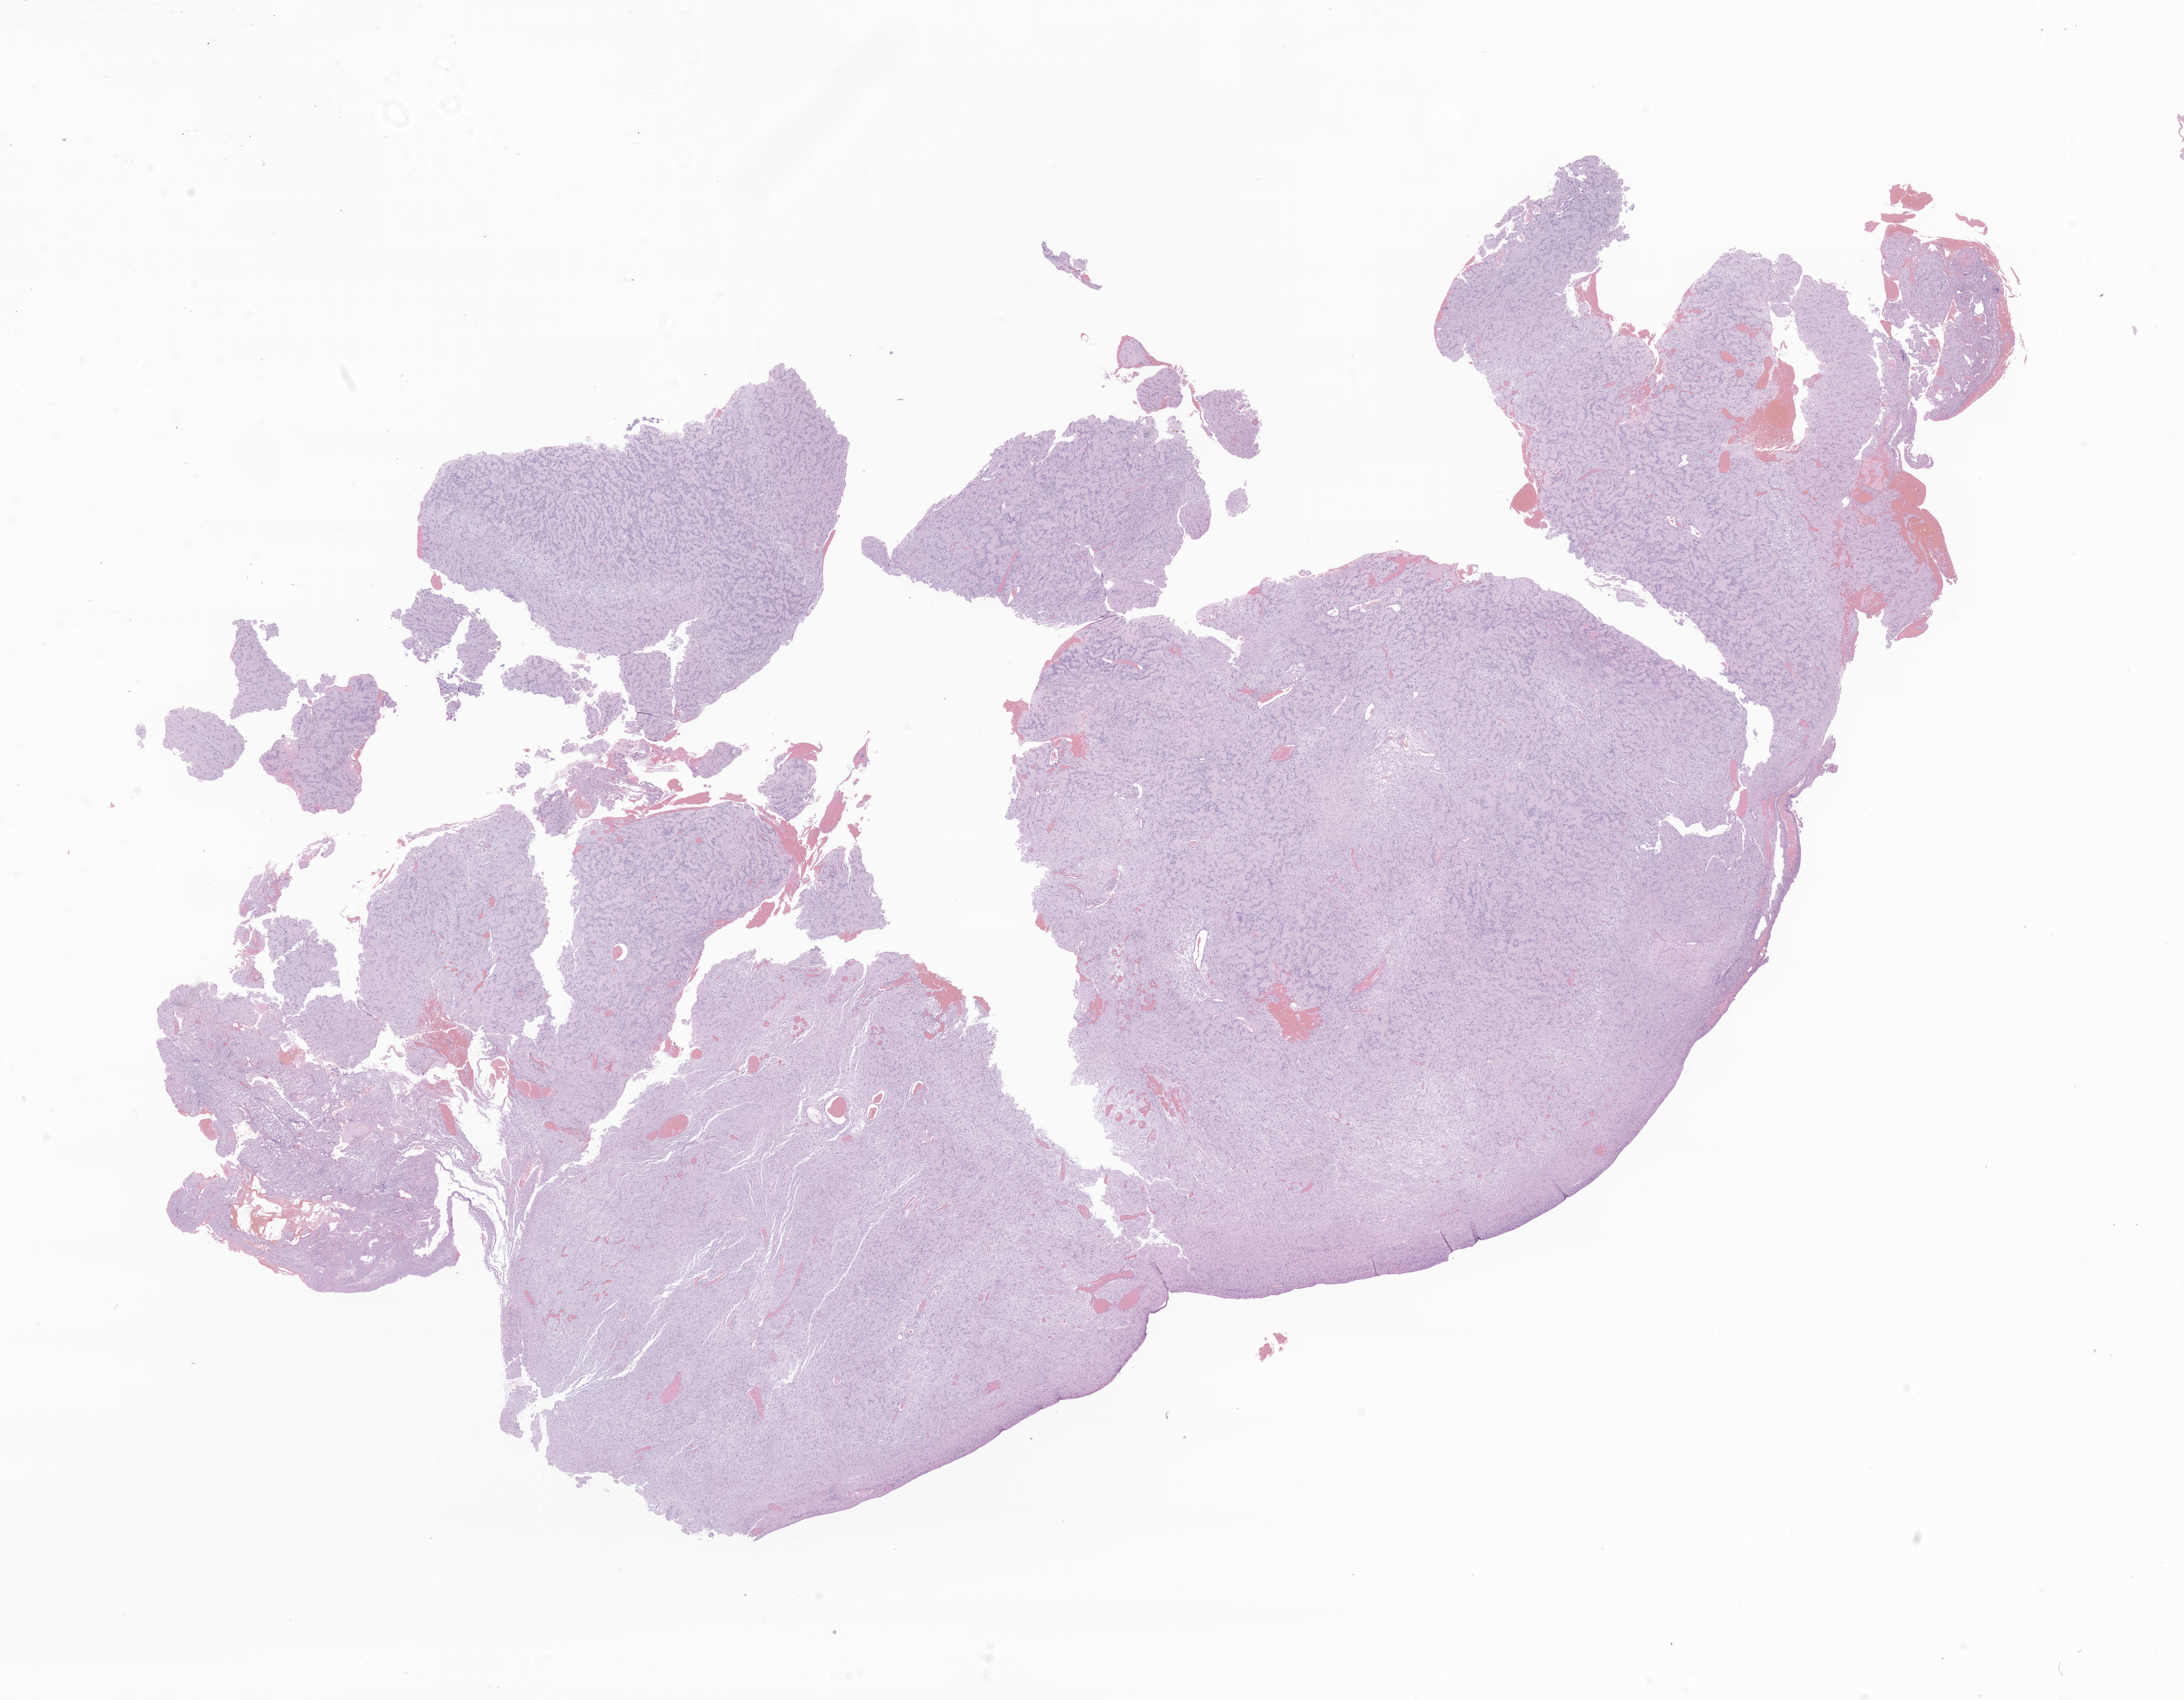
Hematoxylin and eosin (H&E) whole-slide image of tumor tissue from the spinal cord — whole scanned area (about 25.6 x 20.0 mm) shown as a low-resolution overview, formalin-fixed paraffin-embedded section. Patient: female, age 155 months.
* recorded diagnosis: Ganglioneuroma